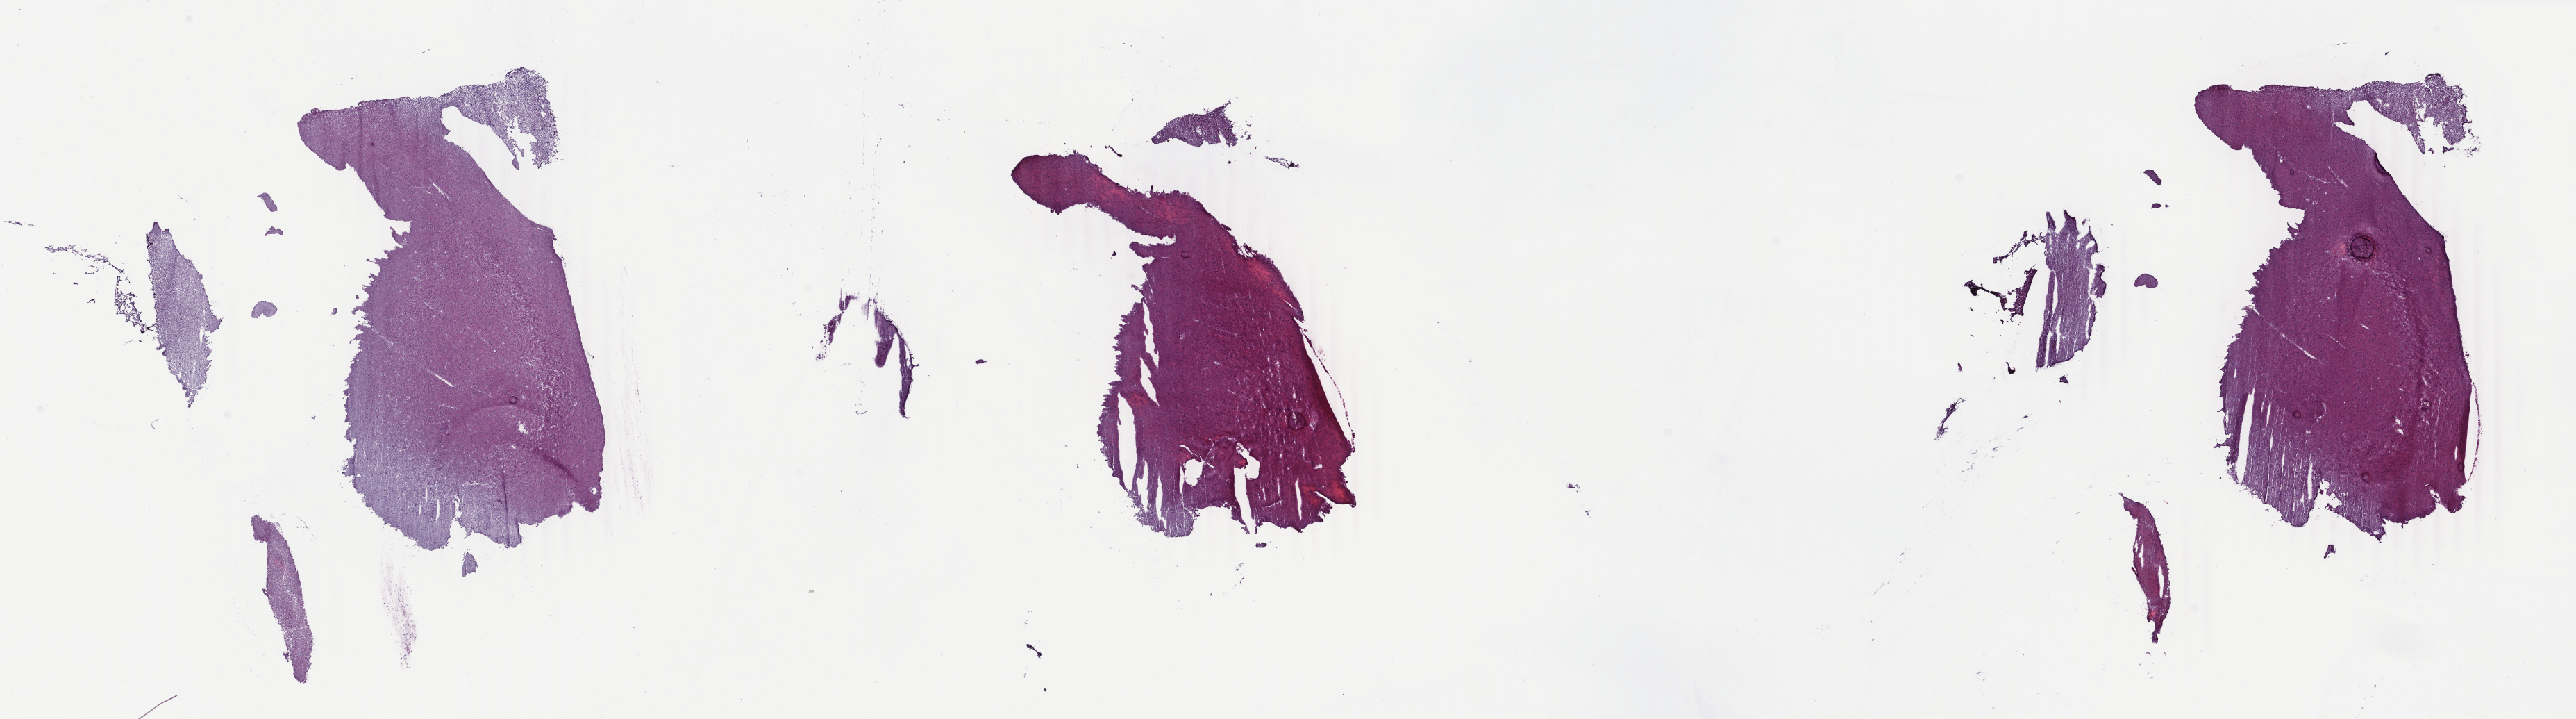
Digitized Hematoxylin and eosin (H&E) stained tissue section (whole slide) — low-resolution overview of the scanned area, about 29.5 x 8.2 mm. Frozen section from the top of the tissue portion. Primary tumour sample from the brain. Female patient; age at initial diagnosis 51 years. Histologic grade: G3 (poorly differentiated). Slide review estimates, as recorded: tumour cells 50%, tumour nuclei 70%, normal cells 50%, stromal cells 0%, necrosis 0%. Infiltration values recorded for this section: lymphocyte infiltration 0%, monocyte infiltration 0%, neutrophil infiltration 0%.
Laterality: left. Pathologic diagnosis: Oligodendroglioma, anaplastic (cerebrum).